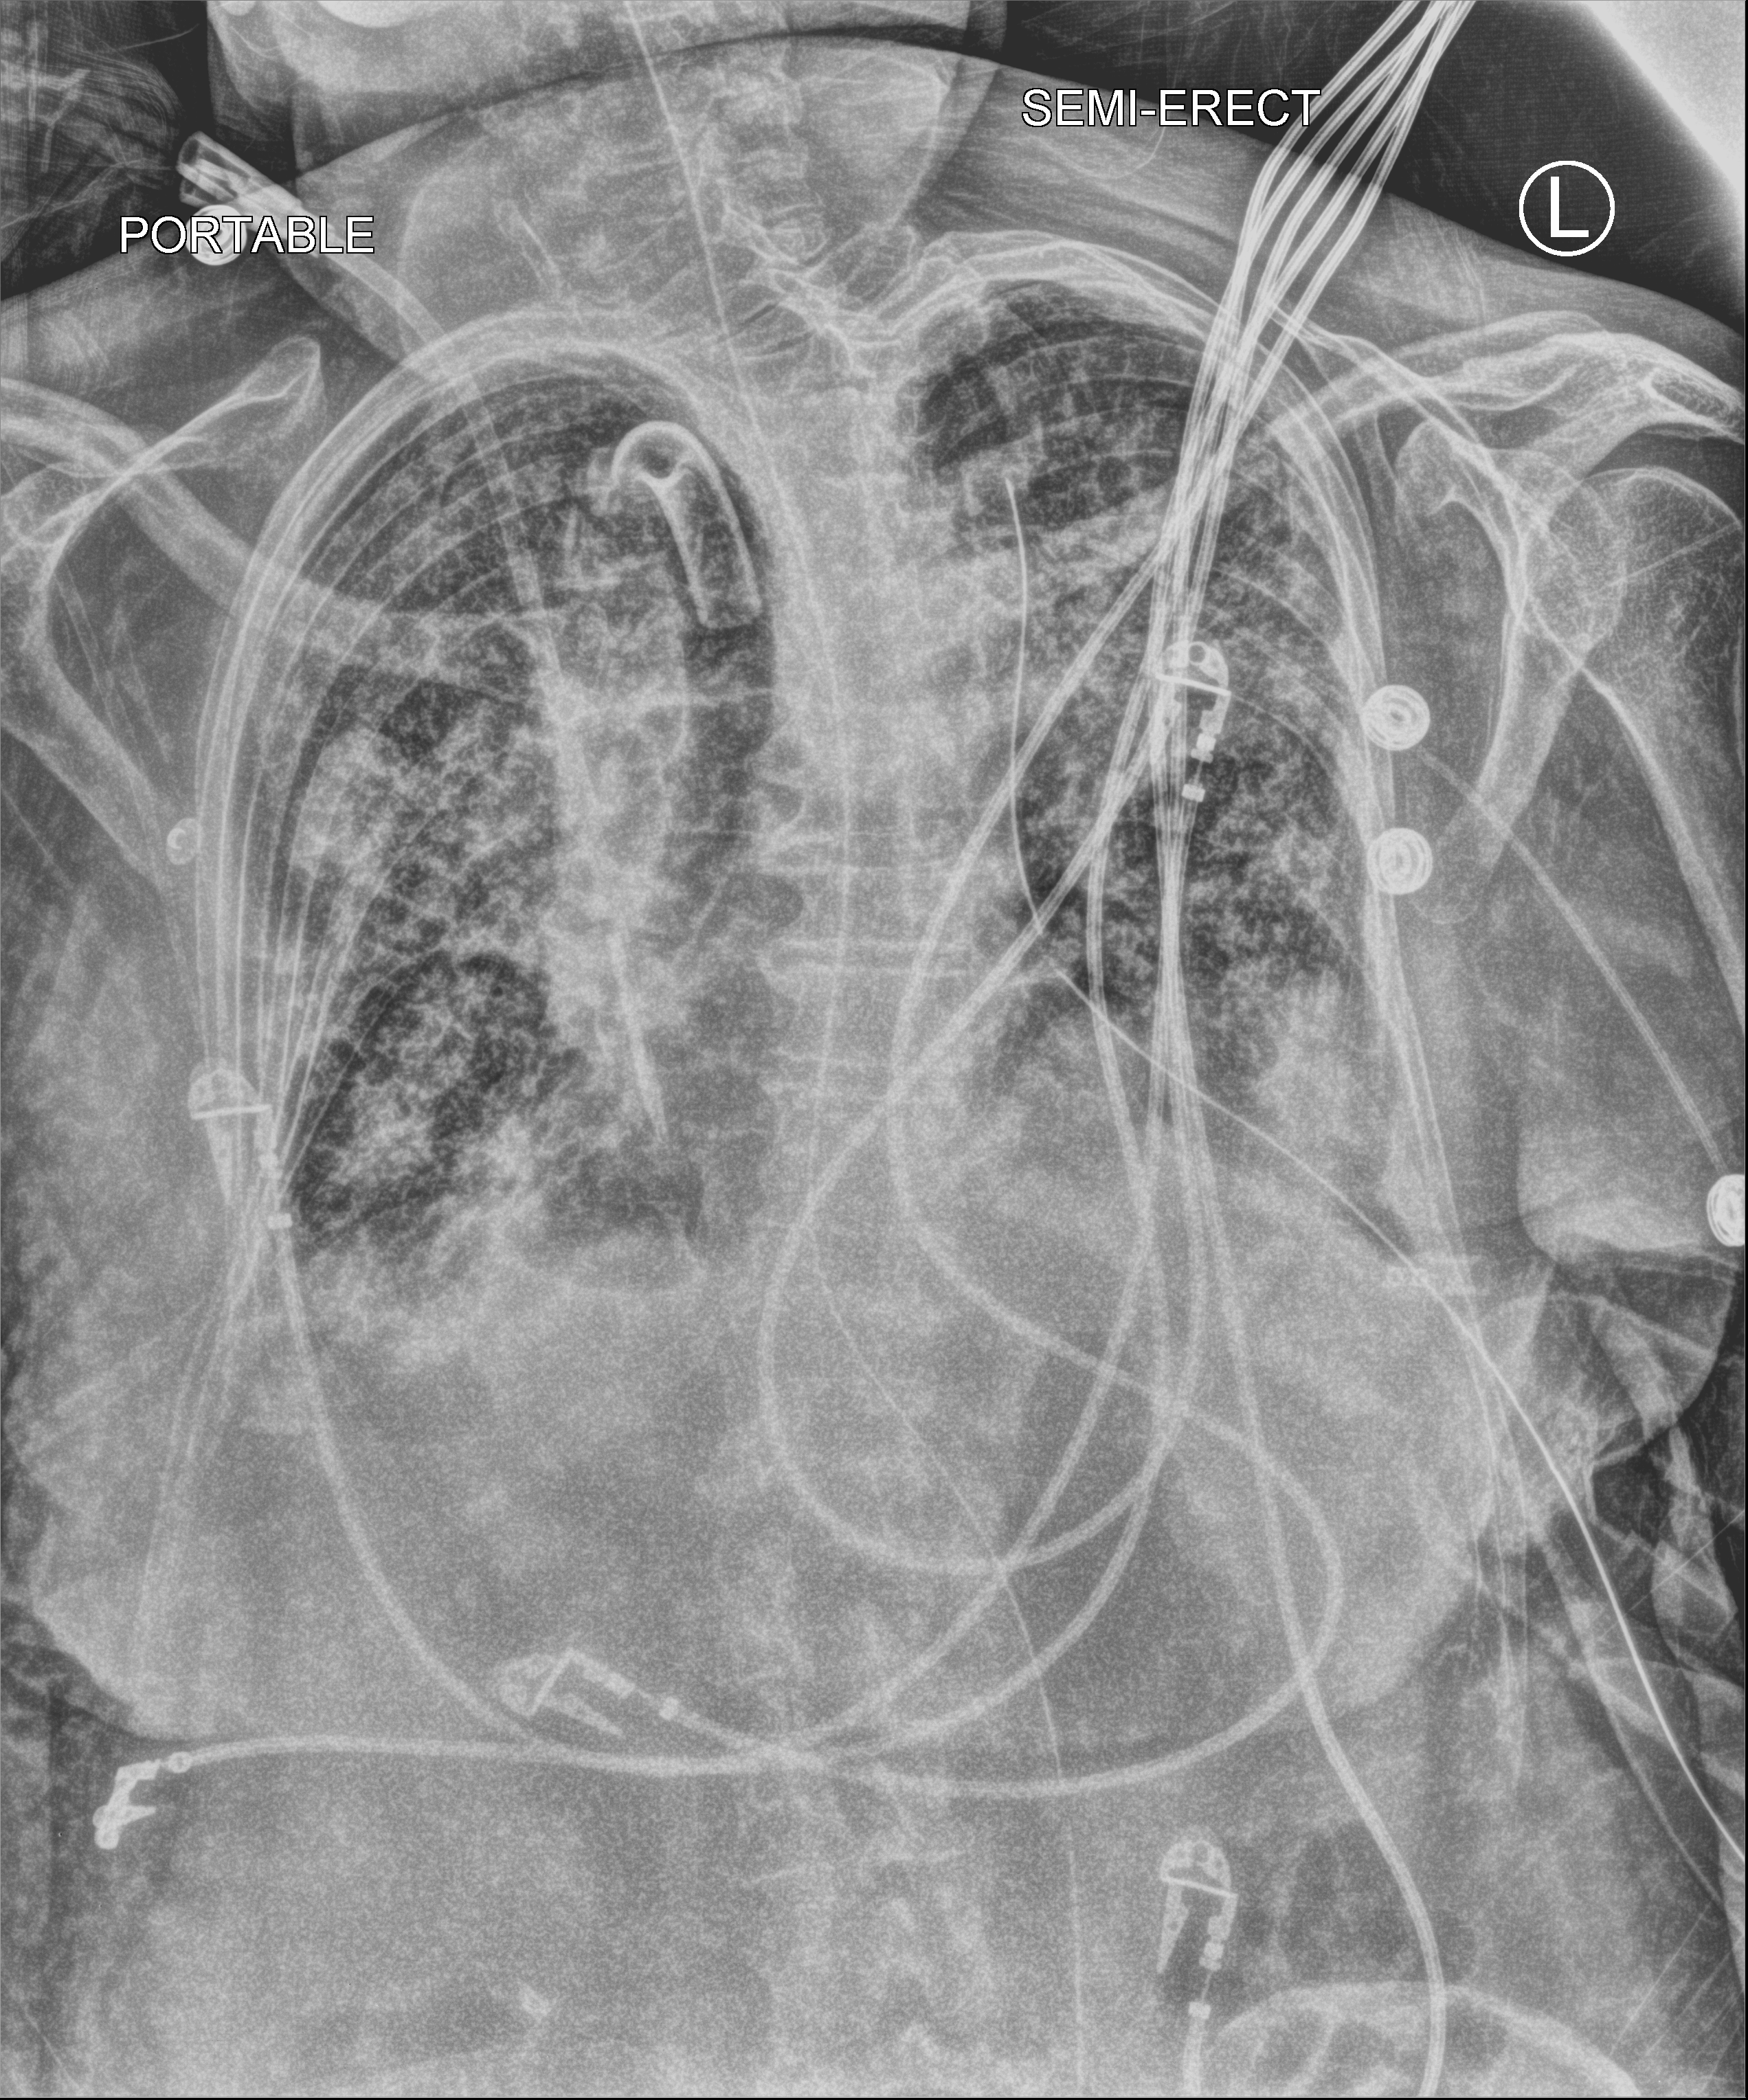
Chest X-ray (portable); anteroposterior (AP) projection. Female patient hospitalised with COVID-19, age 75–90 years.
Hospital-stay facts (about this admission, not read from this image; timing relative to this image not recorded): admitted to intensive care during this hospital stay: yes; mechanically ventilated during this hospital stay: yes.